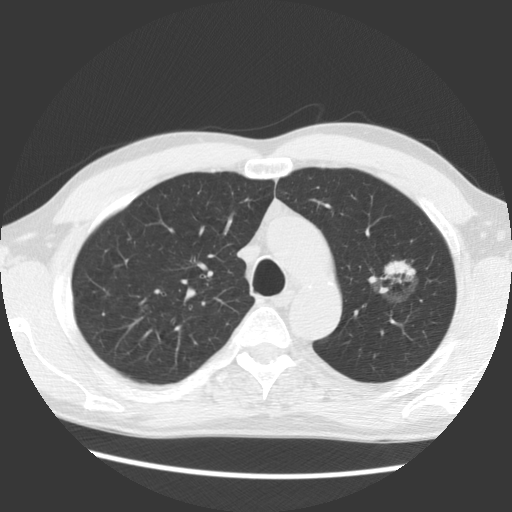
Low-dose screening chest CT, axial slice. Baseline screening round. Lung window (W 1500 / L -600 HU). 2.5 mm slice thickness. Standard (soft-tissue) reconstruction kernel (STANDARD). Slice 100 of 138 in the series. 512 × 512 image matrix. Male participant, aged 61 years at enrolment. Former smoker at enrolment.
Lesion marked by an expert reader, box from (x=355, y=240) to (x=440, y=316) px. The exam's reader record, not a measurement of the box and not confirmed to be the same lesion: non-calcified nodule or mass ≥4 mm, left upper lobe, 17 × 14 mm, soft tissue attenuation. Official screen result: positive, change unspecified: nodule(s) >= 4 mm or enlarging nodule(s), mass(es), or other non-specific abnormalities suspicious for lung cancer. Later outcome: lung cancer diagnosed 1061 days after this screen — bronchiolo-alveolar adenocarcinoma, NOS, left upper lobe, well differentiated (G1), stage IB (AJCC 6th edition), 44 mm at pathology.